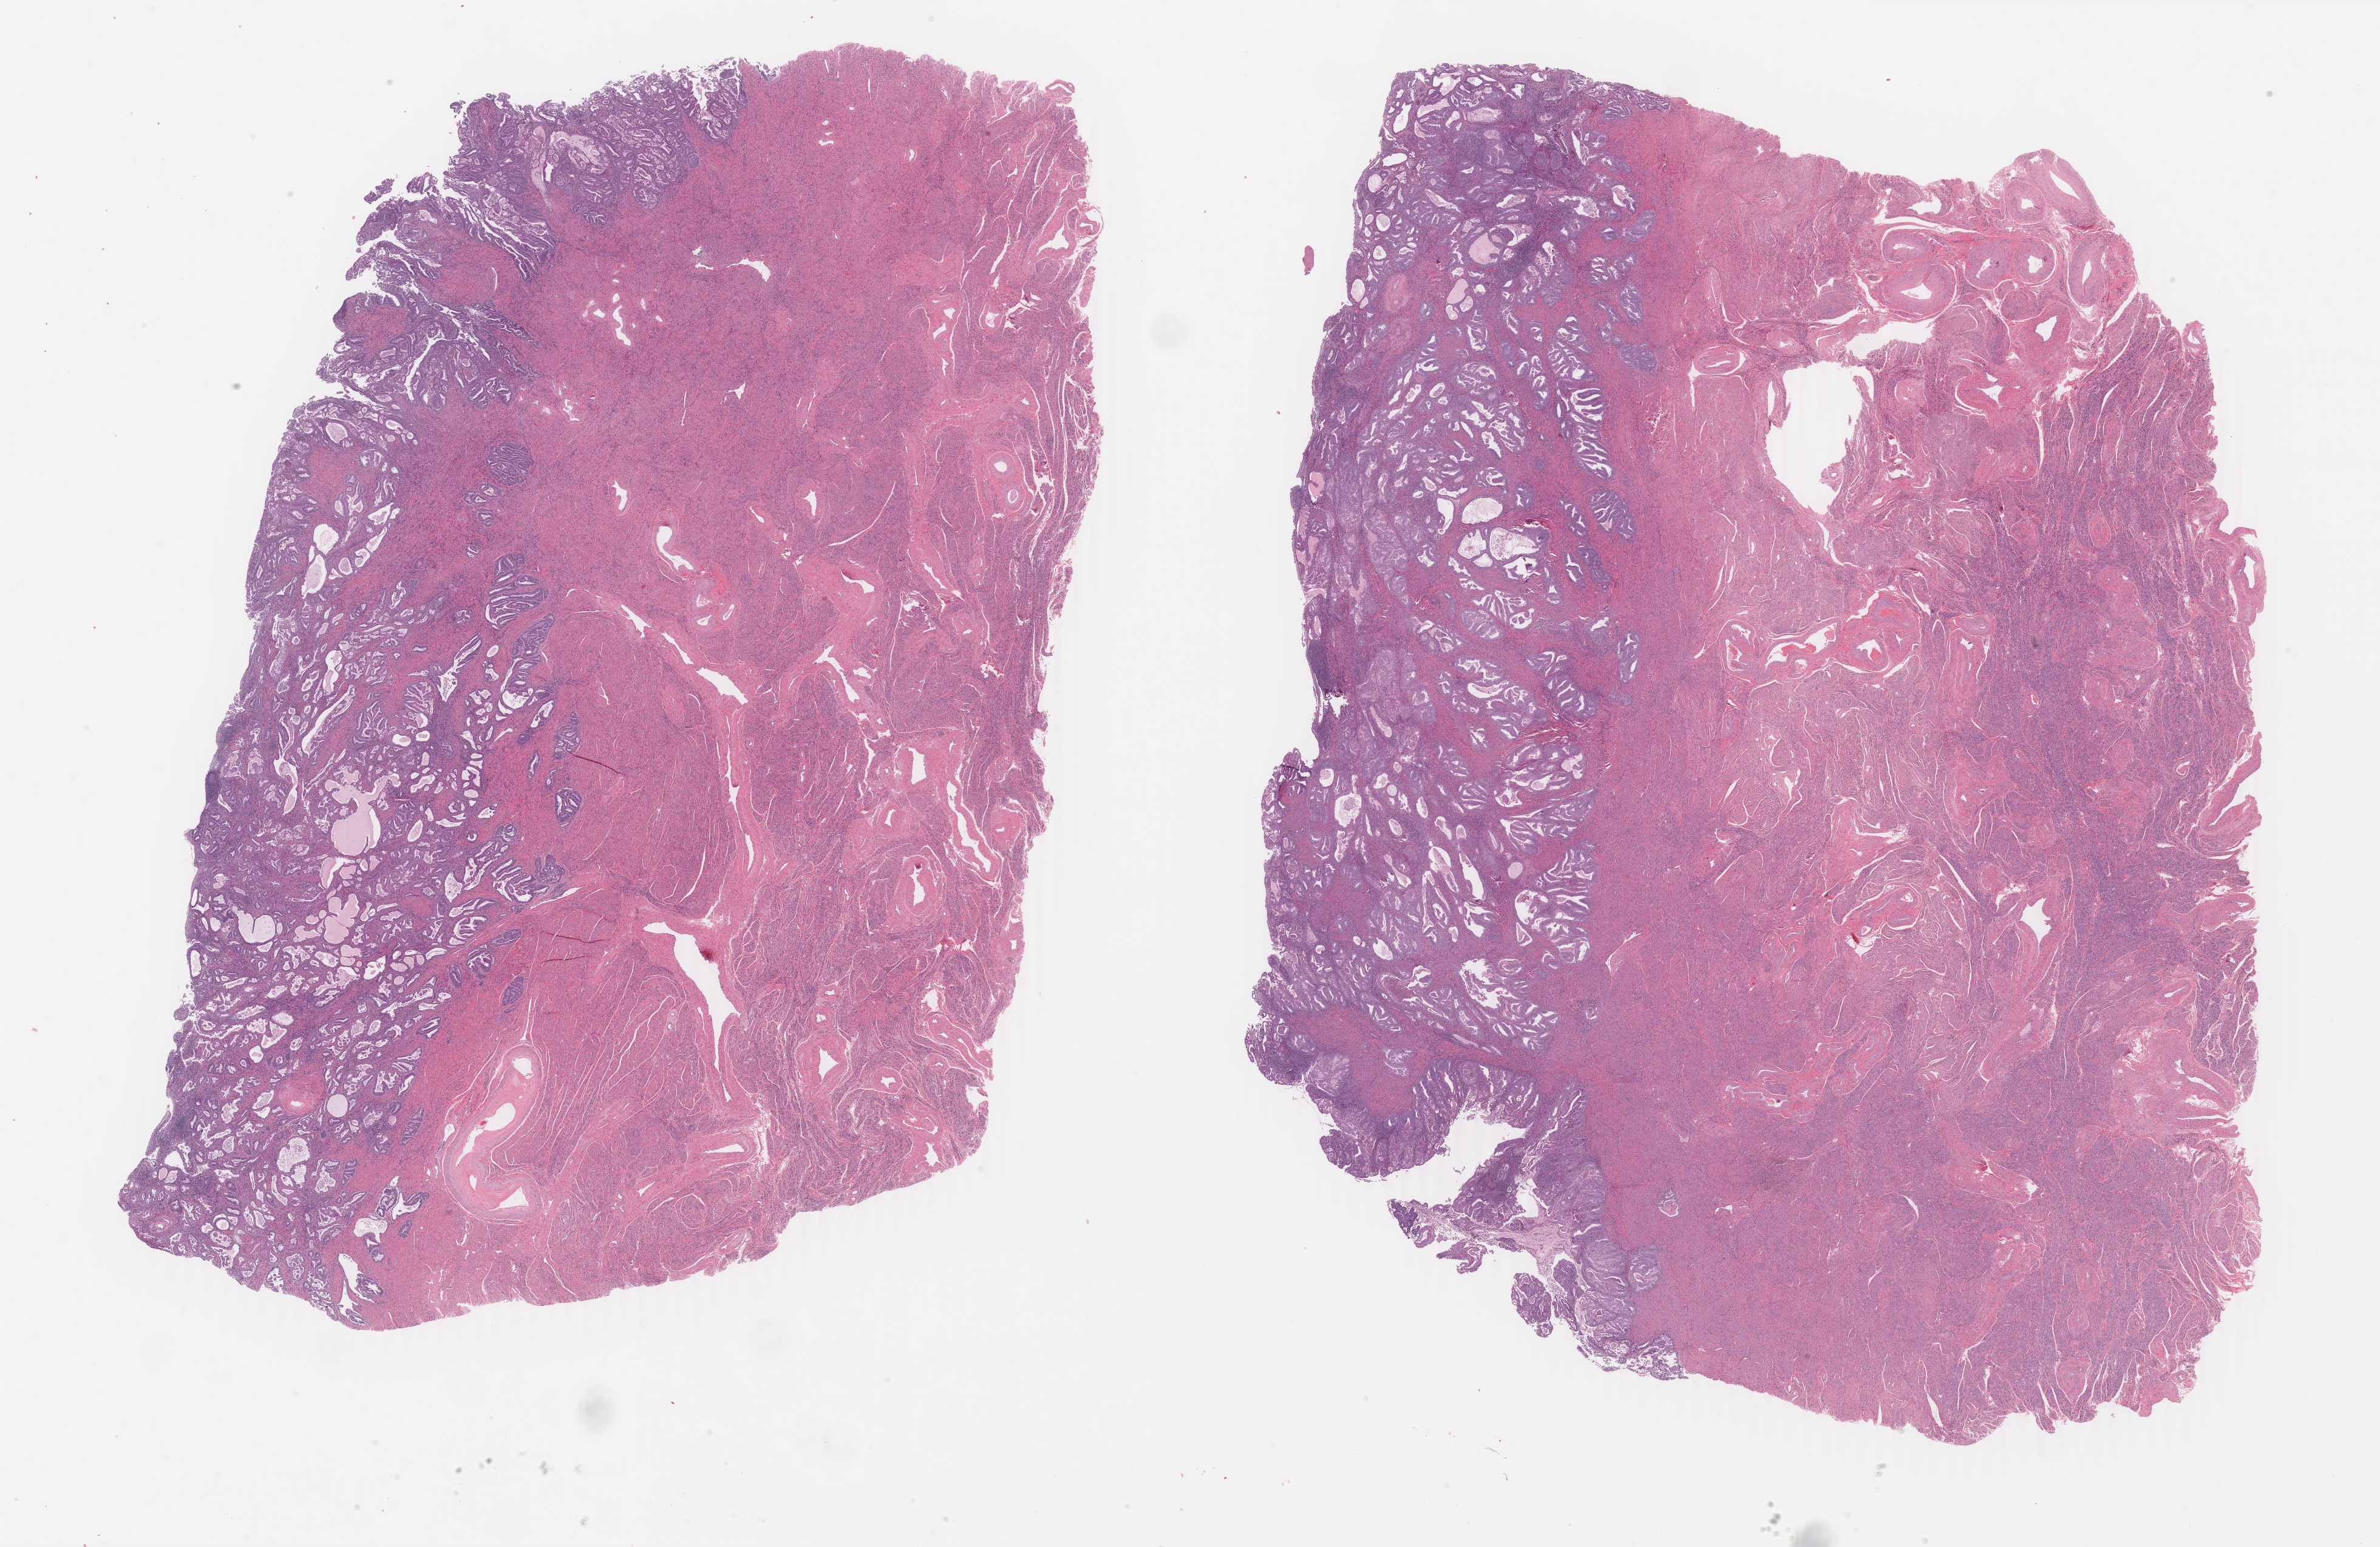
Digitized Hematoxylin and eosin (H&E) stained tissue section (whole slide) — a low-resolution overview of the entire scanned area, about 31.2 x 20.3 mm; formalin-fixed paraffin-embedded (FFPE) diagnostic section; uterus, primary tumour sample. Female patient; age at initial diagnosis 67 years. Histologic grade: G2 (moderately differentiated).
Histologic diagnosis: Endometrioid adenocarcinoma, NOS (endometrium). FIGO stage: IA.